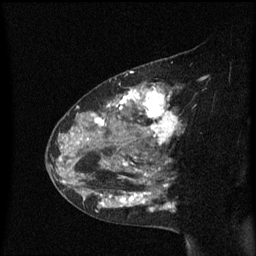
Breast MRI (dynamic contrast-enhanced), one sagittal slice. Slice 39 of 60 in the series (ordered by position). Dynamic contrast-enhanced series, image 2 of 3 at this slice position (ordered by acquisition). 1.5 T. TE 4.2 ms, TR 8.4 ms. 2 mm slice thickness. 256 × 256 image matrix, field of view 200 × 200 mm. Female patient, age 48 years. From the clinical record (not read from this slice): setting: breast cancer imaged before/during neoadjuvant chemotherapy; receptor status: HR-positive, HER2-negative.
Structures marked on this image (semi-automatic segmentation, software-assisted and operator-edited):
- analysis volume of interest (the breast-tissue region the enhancement analysis was run in; not a lesion): bounding box [x1, y1, x2, y2] px = [80, 78, 185, 221]
- tumour enhancement mask (voxels above the 70 % enhancement threshold inside the analysis volume of interest): [92, 86, 181, 211]